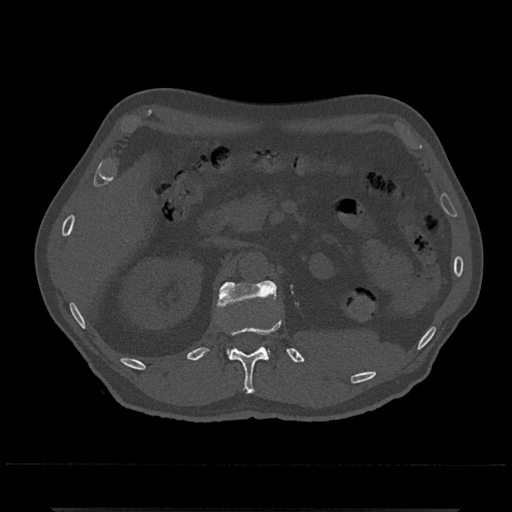
CT including the spine, one axial slice; position 405 of 797 along the scan axis; 120 kVp; bone window (W 1800 / L 400 HU); 0.5 mm slice thickness; 512 × 512 image matrix, field of view 393 × 393 mm. Patient: male, 67 years. Case-level facts recorded for this patient, not image findings: primary cancer: prostate.
Structures marked on this image (semi-automatically segmented with operator editing):
- L1 vertebra: bounding box (x1, y1, x2, y2) in pixels: (217, 280, 277, 359)
- T12 vertebra: (229, 321, 281, 394)